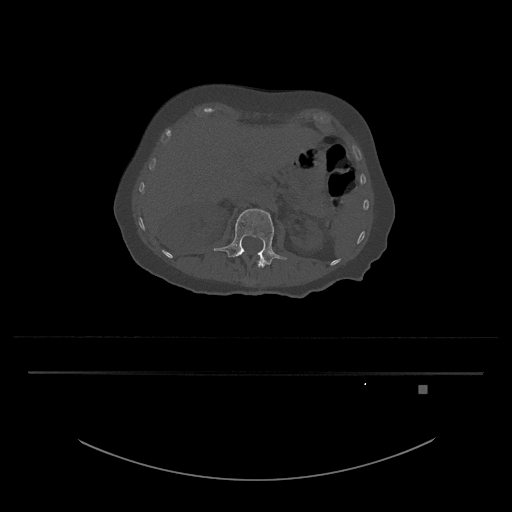
CT including the spine, one axial slice. Position 505 of 797 along the scan axis. 120 kVp. Bone window (W 1800 / L 400 HU). 512 × 512 image matrix. Patient: female, 57 years. From the clinical record (not read from this slice): primary cancer: cervical.
Annotated regions visible in this slice (semi-automatic segmentation, software-assisted and operator-edited):
- L1 vertebra: bounding box [x1, y1, x2, y2] px = [244, 250, 265, 267]